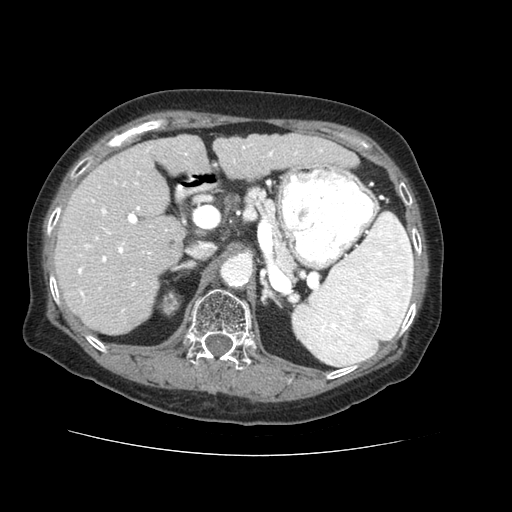
Contrast-enhanced abdominal CT (liver protocol), one axial slice. Slice 33 of 73 in the series (ordered by position). Soft-tissue window (W 400 / L 40 HU). 2.5 mm slice thickness. 512 × 512 image matrix, field of view 360 × 360 mm. From the clinical record (not read from this slice): diagnosis: hepatocellular carcinoma (patient treated with transarterial chemoembolisation; whether this scan precedes or follows treatment is not stated here); TNM stage (as recorded): Stage-IVB; Child-Pugh class: A; tumour differentiation: well differentiated.
Annotated regions visible in this slice (semi-automatic segmentation, software-assisted and operator-edited):
- liver parenchyma outside the tumour (the mass and vessels are separate outlines, so this box may not span the whole liver): bounding box <54,134,358,334> (left, top, right, bottom; pixels)
- liver vessels: <78,143,323,312>